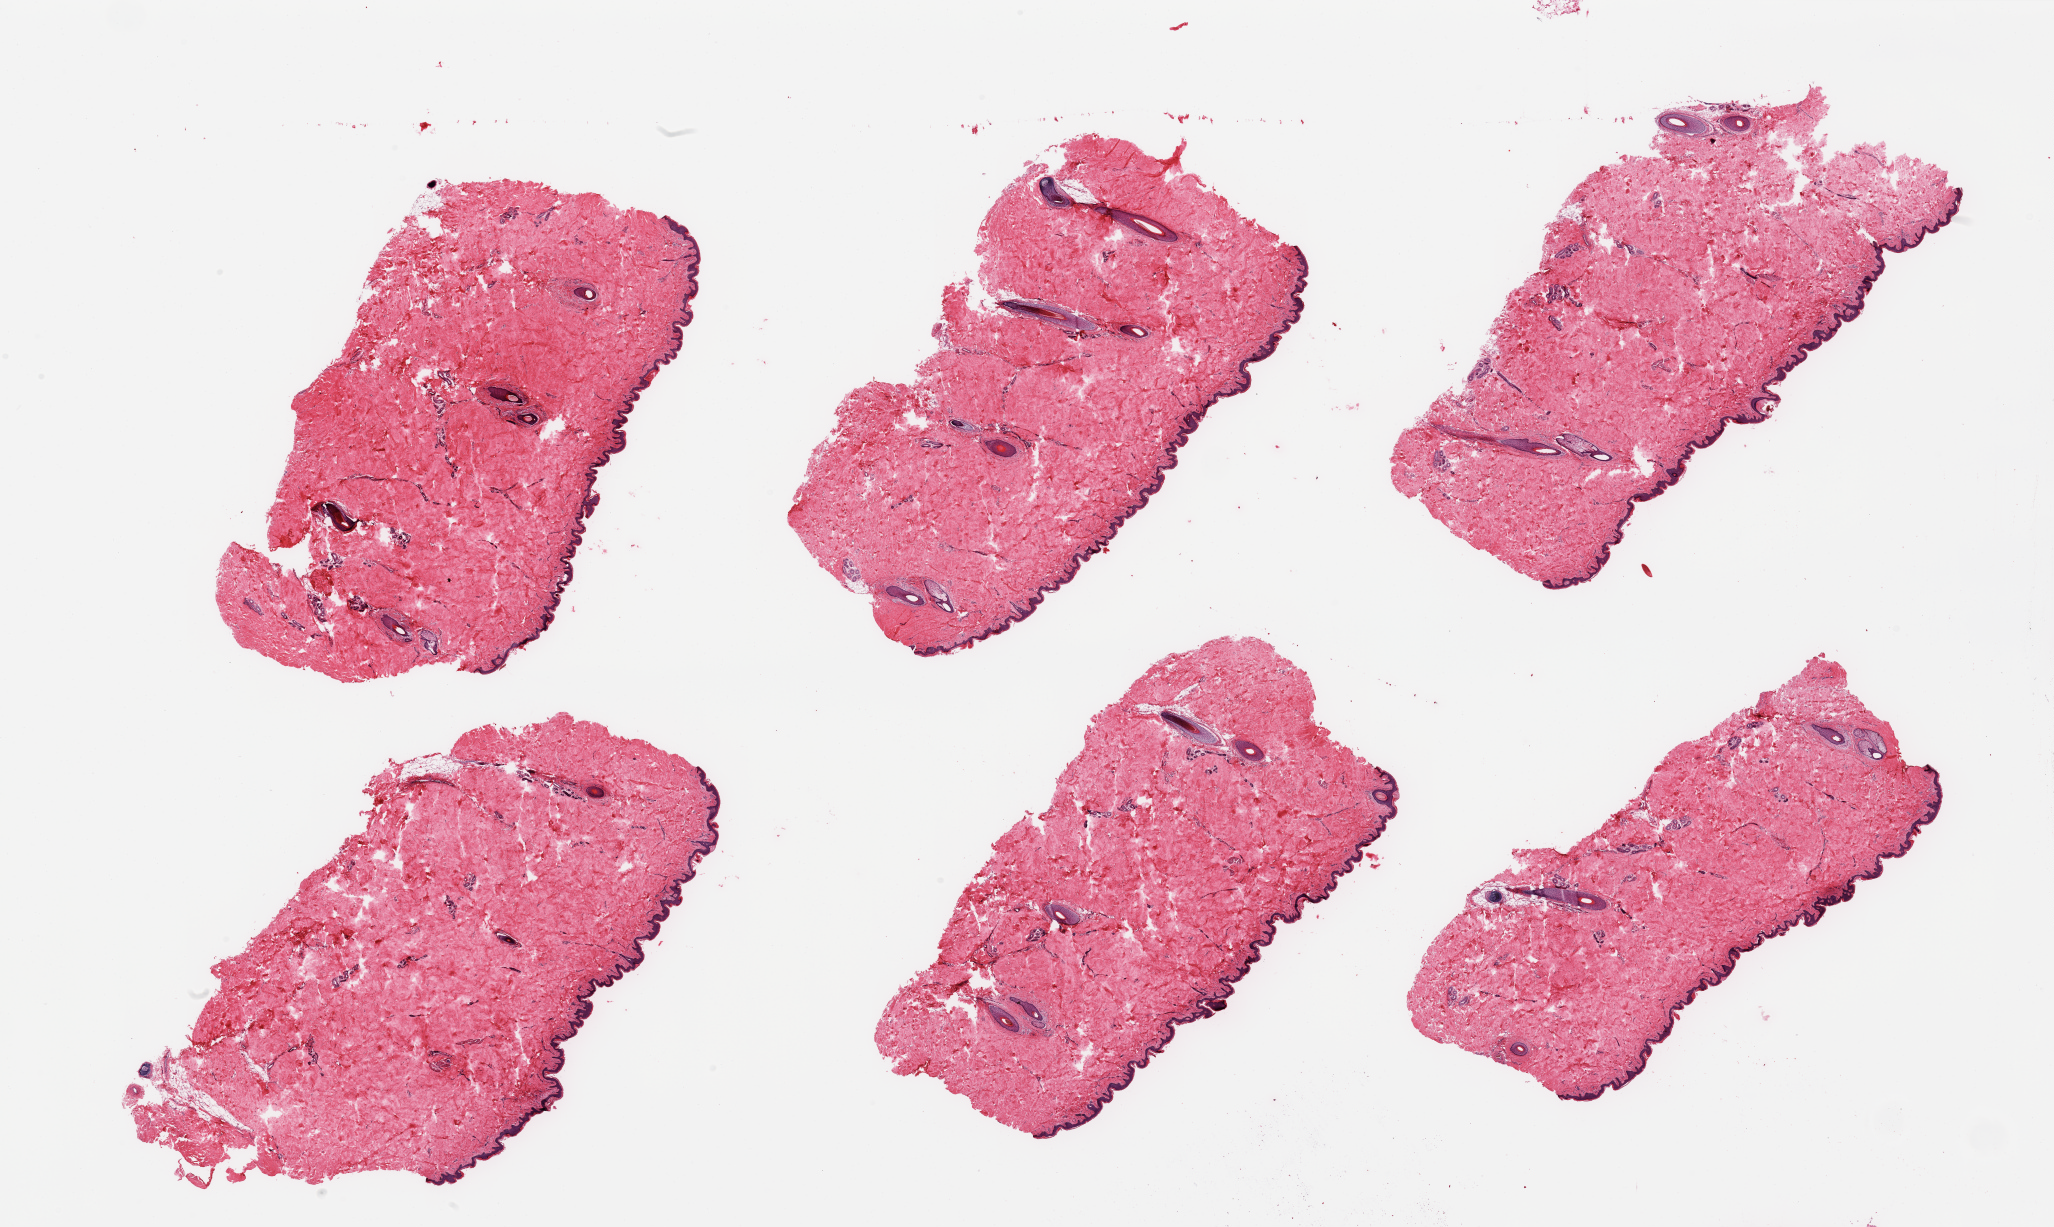
H&E whole-slide image, shown as a low-resolution overview of the whole scanned area (about 32.5 x 19.4 mm), PAXgene-fixed paraffin-embedded (PFPE) section, sampled site (target tissue): skin of suprapubic region, donor tissue sample. Male donor.
* pathologist's review note for this sample: 6 pieces; well trimmed hair-bearing skin